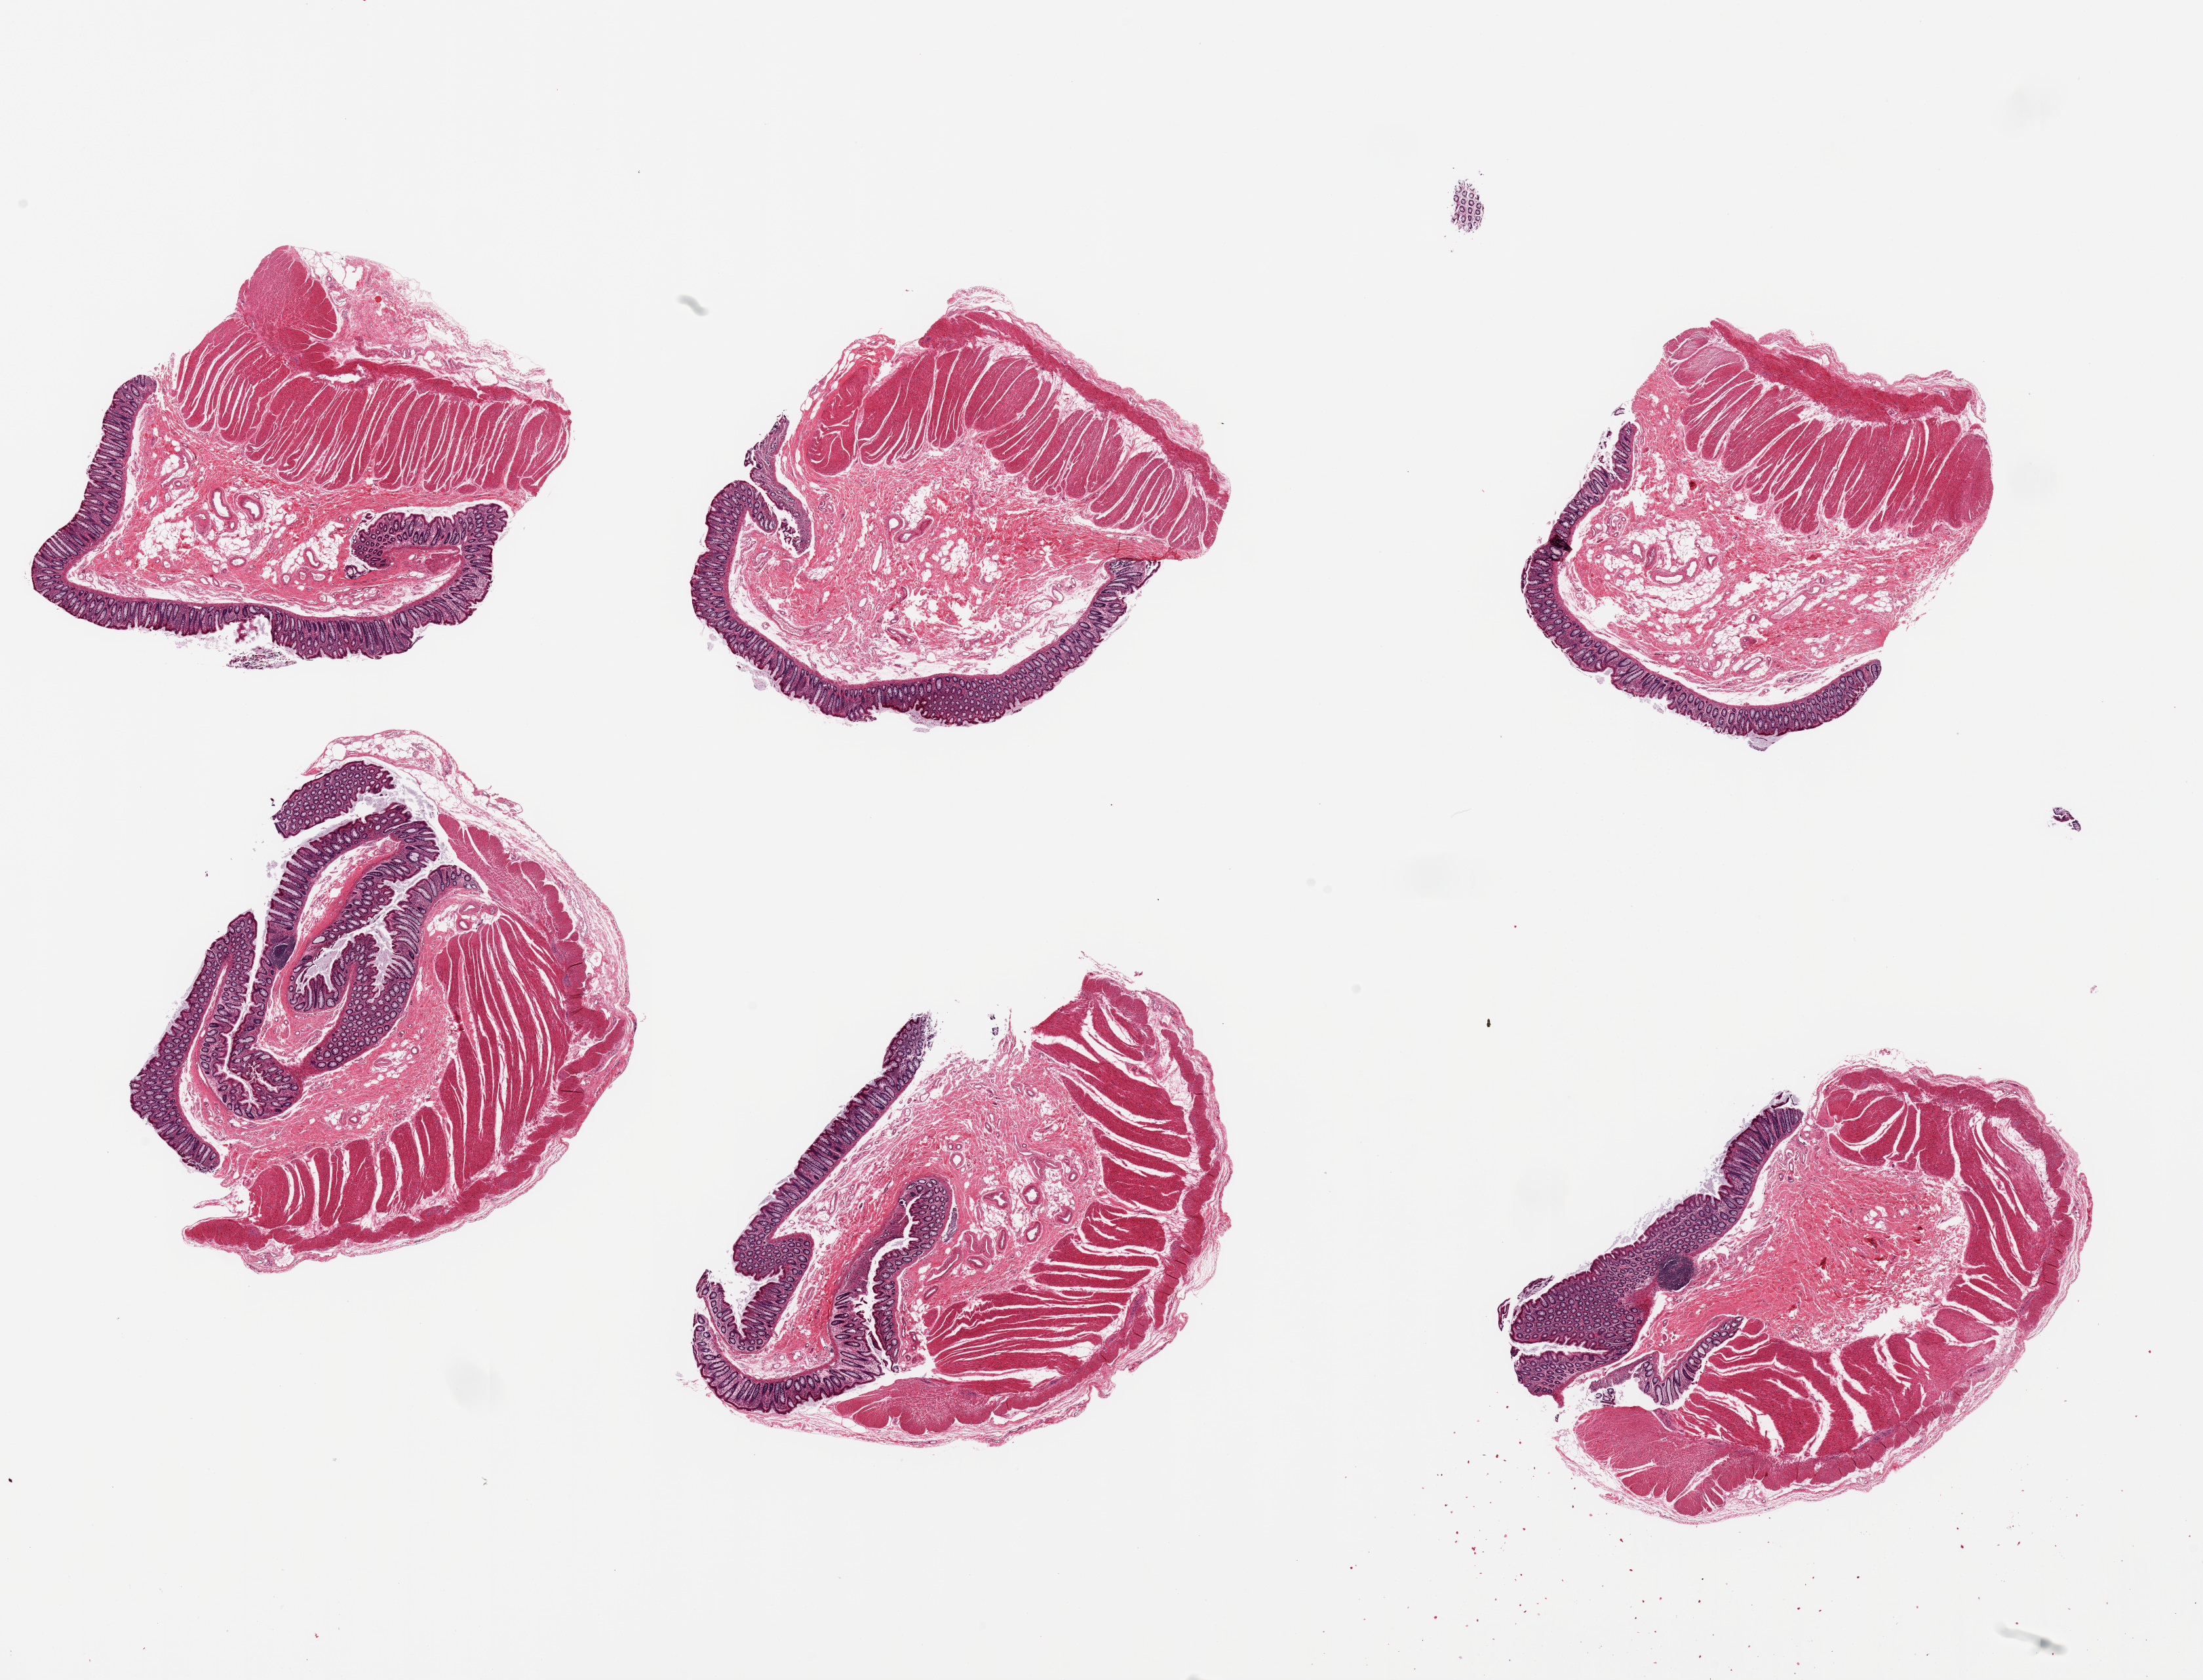
Whole-slide image, hematoxylin and eosin (H&E) stain — low-resolution overview of the scanned area, about 26.6 x 20.3 mm, PAXgene-fixed, paraffin-embedded tissue, sampled site (target tissue): transverse colon, donor tissue sample. Donor sex: male.
Reviewer comment on this tissue sample: 6 pieces, mucosa unusually well preserved, ~0.5mm, ~10% thickness.